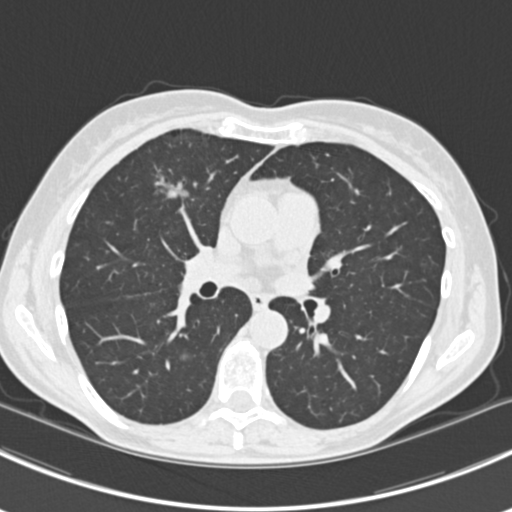
Low-dose screening chest CT, axial slice; first (baseline) screen; lung window (W 1500 / L -600 HU); 2 mm slice thickness; slice 85 of 224 in the series; 512 × 512 image matrix, field of view 310 × 310 mm. Female participant, aged 63 years at enrolment.
Lesion marked by an expert reader, bounding box [x1, y1, x2, y2] px = [144, 162, 203, 218]. The screening reader recorded 10 non-calcified nodules or masses ≥4 mm on this exam (right lower lobe, right lower lobe, left lower lobe, left lower lobe, right middle lobe, right lower lobe, left lower lobe, left upper lobe, right upper lobe, left upper lobe); which of them this box marks is not recorded.